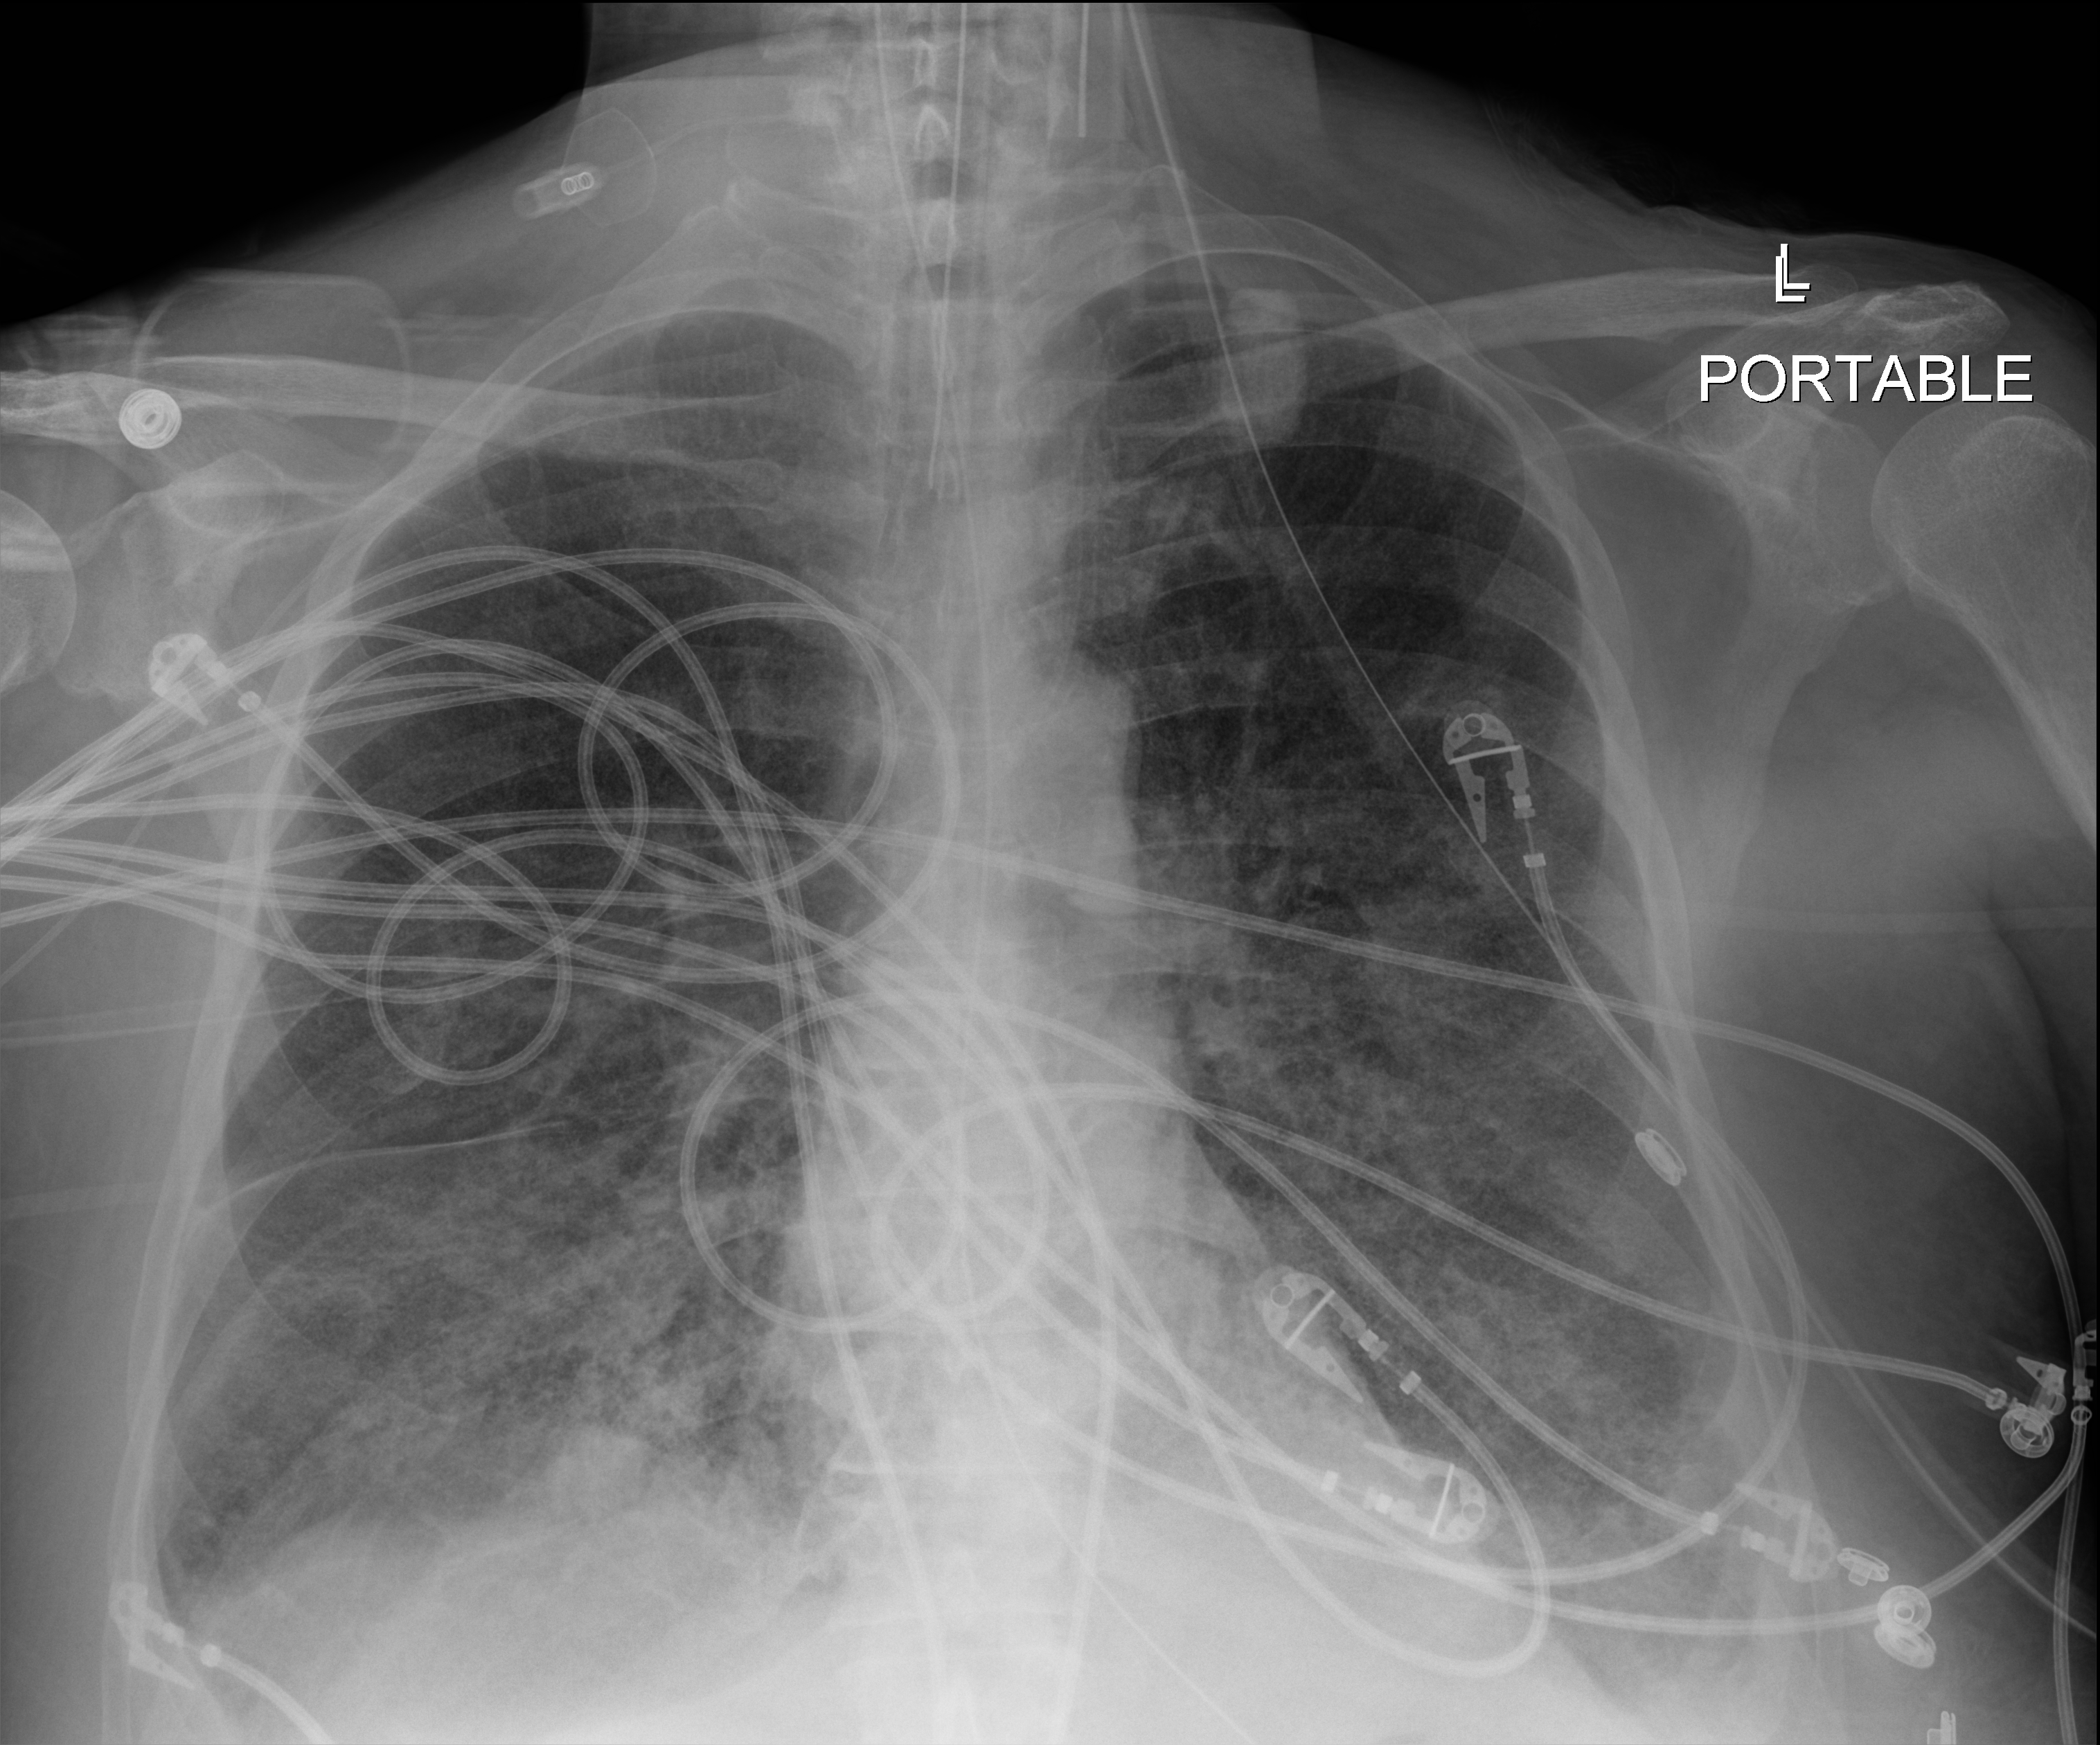
Portable chest radiograph; anteroposterior (AP) projection. Patient hospitalised with COVID-19; male, aged 60–74 years.
Admission-level facts for this patient (not findings on this image; timing relative to this image not recorded):
- COPD (admission record): no
- other chronic lung disease (admission record): no